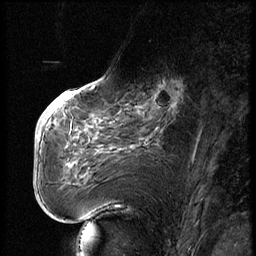
Breast MRI (dynamic contrast-enhanced), one sagittal slice; position 27 of 74 along the scan axis; dynamic contrast-enhanced series, image 2 of 3 at this slice position (ordered by acquisition); 1.5 T; TE 4.2 ms, TR 9 ms; 256 × 256 image matrix, field of view 180 × 180 mm. Patient: female, 56 years. From the clinical record (not read from this slice): setting: breast cancer imaged before/during neoadjuvant chemotherapy.
Outlined on this slice (semi-automatically segmented with operator editing):
- analysis volume of interest (the breast-tissue region the enhancement analysis was run in; not a lesion): bounding box (x1, y1, x2, y2) in pixels: (123, 71, 195, 131)
- tumour enhancement mask (voxels above the 140 % enhancement threshold inside the analysis volume of interest): (150, 79, 183, 113)